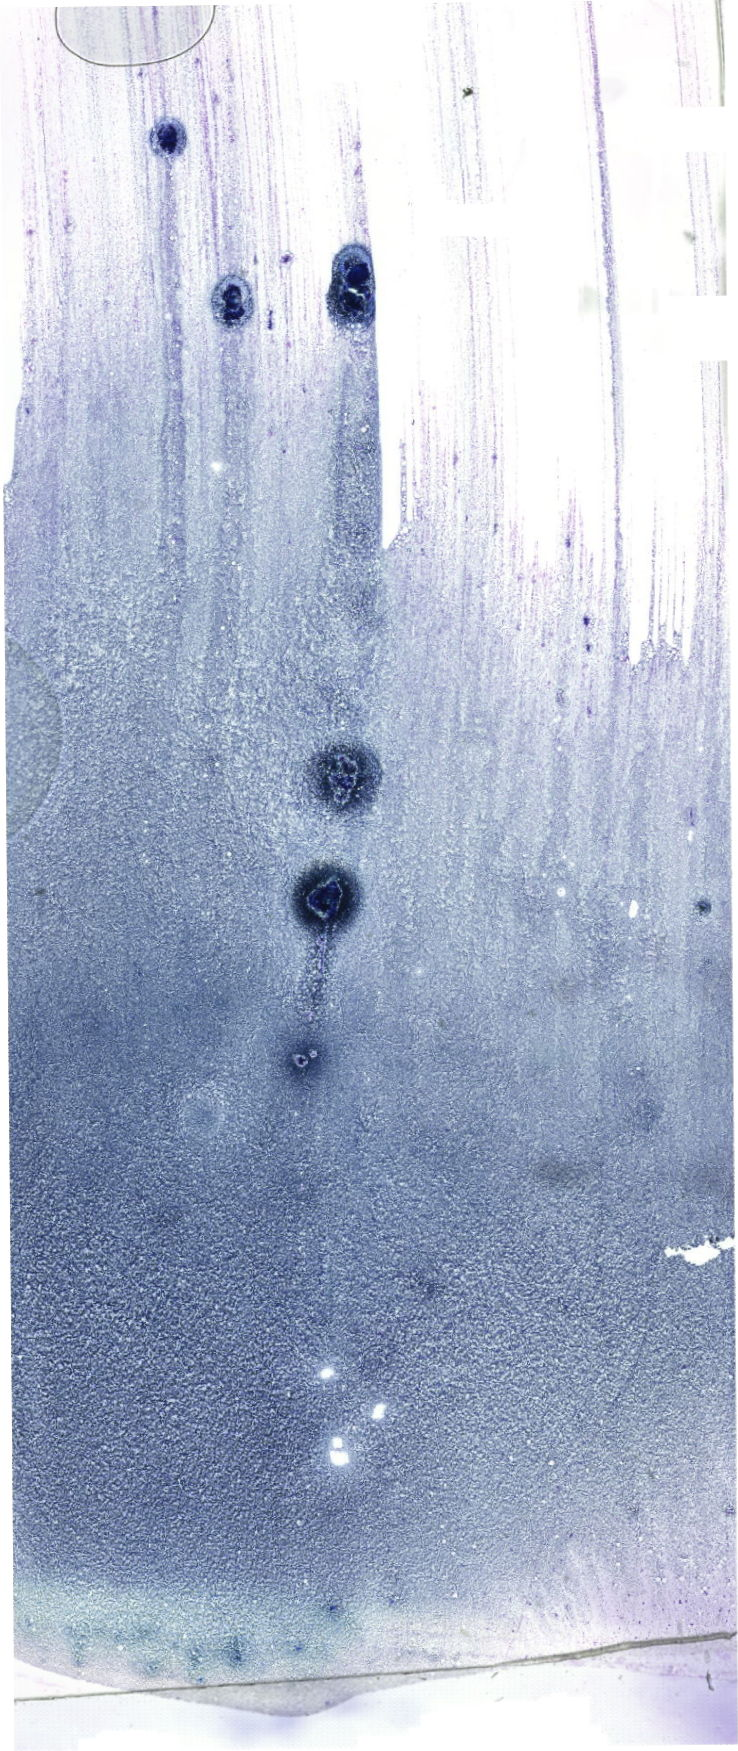
Whole-slide image of a May-Grünwald-Giemsa (MGG)-stained bone marrow aspirate smear, a low-resolution overview of the entire scanned area, about 20.9 x 49.6 mm. Male patient.
- diagnosis: B Acute Lymphoblastic Leukemia